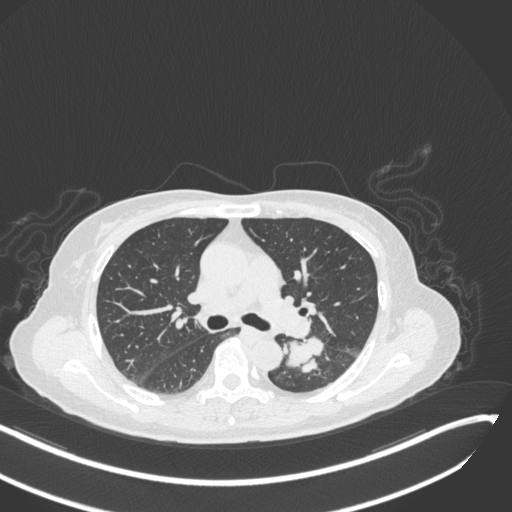
Chest CT, one axial slice; slice 174 of 342 in the series (ordered by position); reconstruction kernel B31f; lung window (W 1500 / L -600 HU); 1 mm slice thickness; 512 × 512 image matrix, field of view 400 × 400 mm. Patient: female, 64 years. Case-level facts recorded for this patient, not image findings: clinical TNM (as recorded): T3 N1 M1.
Outlined on this slice (rectangle marked by the reading radiologist):
- lung tumour (recorded histology: small cell carcinoma): bounding box (x1, y1, x2, y2) in pixels: (283, 333, 326, 374)